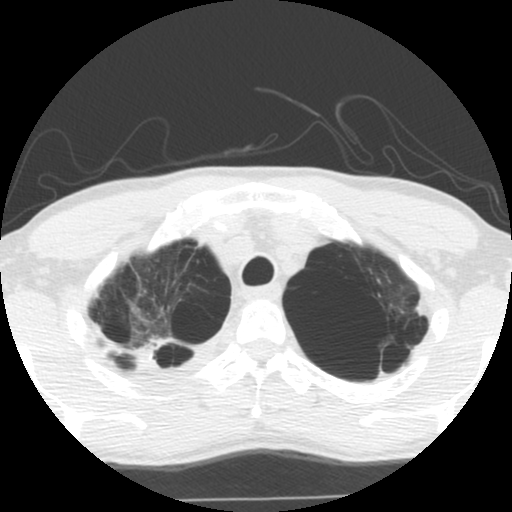
Low-dose screening chest CT, one axial slice; slice 99 of 119 in the series (ordered by position); reconstruction kernel STANDARD; 140 kVp; lung window (W 1500 / L -600 HU); 2.5 mm slice thickness; 512 × 512 image matrix.
Annotated regions visible in this slice (expert manual segmentation):
- lesion 1 (tumor, upper lobe of right lung): box from (x=119, y=335) to (x=172, y=370) px